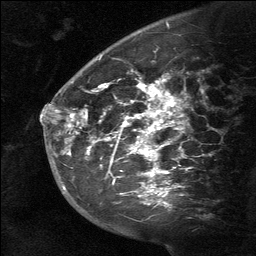
Breast MRI (dynamic contrast-enhanced), one sagittal slice; position 44 of 64 along the scan axis; dynamic contrast-enhanced study with each time point stored as its own series, time point 2 of 3 at this slice position (early post-contrast, ordered by acquisition time); 1.5 T; TE 4.8 ms, TR 27 ms; 2 mm slice thickness; 256 × 256 image matrix, field of view 180 × 180 mm. Patient: female, 39 years. Case-level facts recorded for this patient, not image findings: setting: breast cancer imaged before/during neoadjuvant chemotherapy; receptor status: HER2-positive.
Structures marked on this image (semi-automatic segmentation, software-assisted and operator-edited):
- analysis volume of interest (the breast-tissue region the enhancement analysis was run in; not a lesion): bounding box [x1, y1, x2, y2] px = [58, 40, 199, 217]
- tumour enhancement mask (voxels above the 90 % enhancement threshold inside the analysis volume of interest): [68, 79, 181, 196]